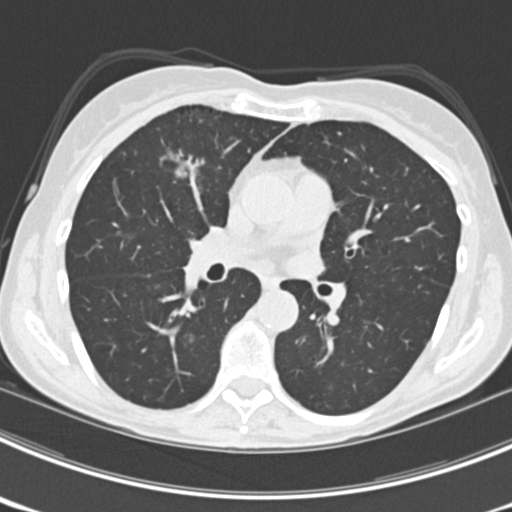
Chest CT (low-dose screening protocol), one axial image, third annual screen, lung window (W 1500 / L -600 HU), 512 × 512 image matrix. Female participant, aged 63 years at enrolment. Current smoker at enrolment.
• Lesion marked by an expert reader, bounding box <153,136,220,196> (left, top, right, bottom; pixels).
• The screening reader recorded 9 non-calcified nodules or masses ≥4 mm on this exam (left upper lobe, right upper lobe, left upper lobe, left lower lobe, right middle lobe, left lower lobe, left lower lobe, right lower lobe, right lower lobe); which of them this box marks is not recorded.
• Official screen result: positive, other.
• Later outcome: lung cancer diagnosed 15 days after this screen — bronchiolo-alveolar adenocarcinoma, NOS, right upper lobe, right middle lobe, right lower lobe, left upper lobe, left lower lobe, moderately differentiated (G2), stage IV (AJCC 6th edition).